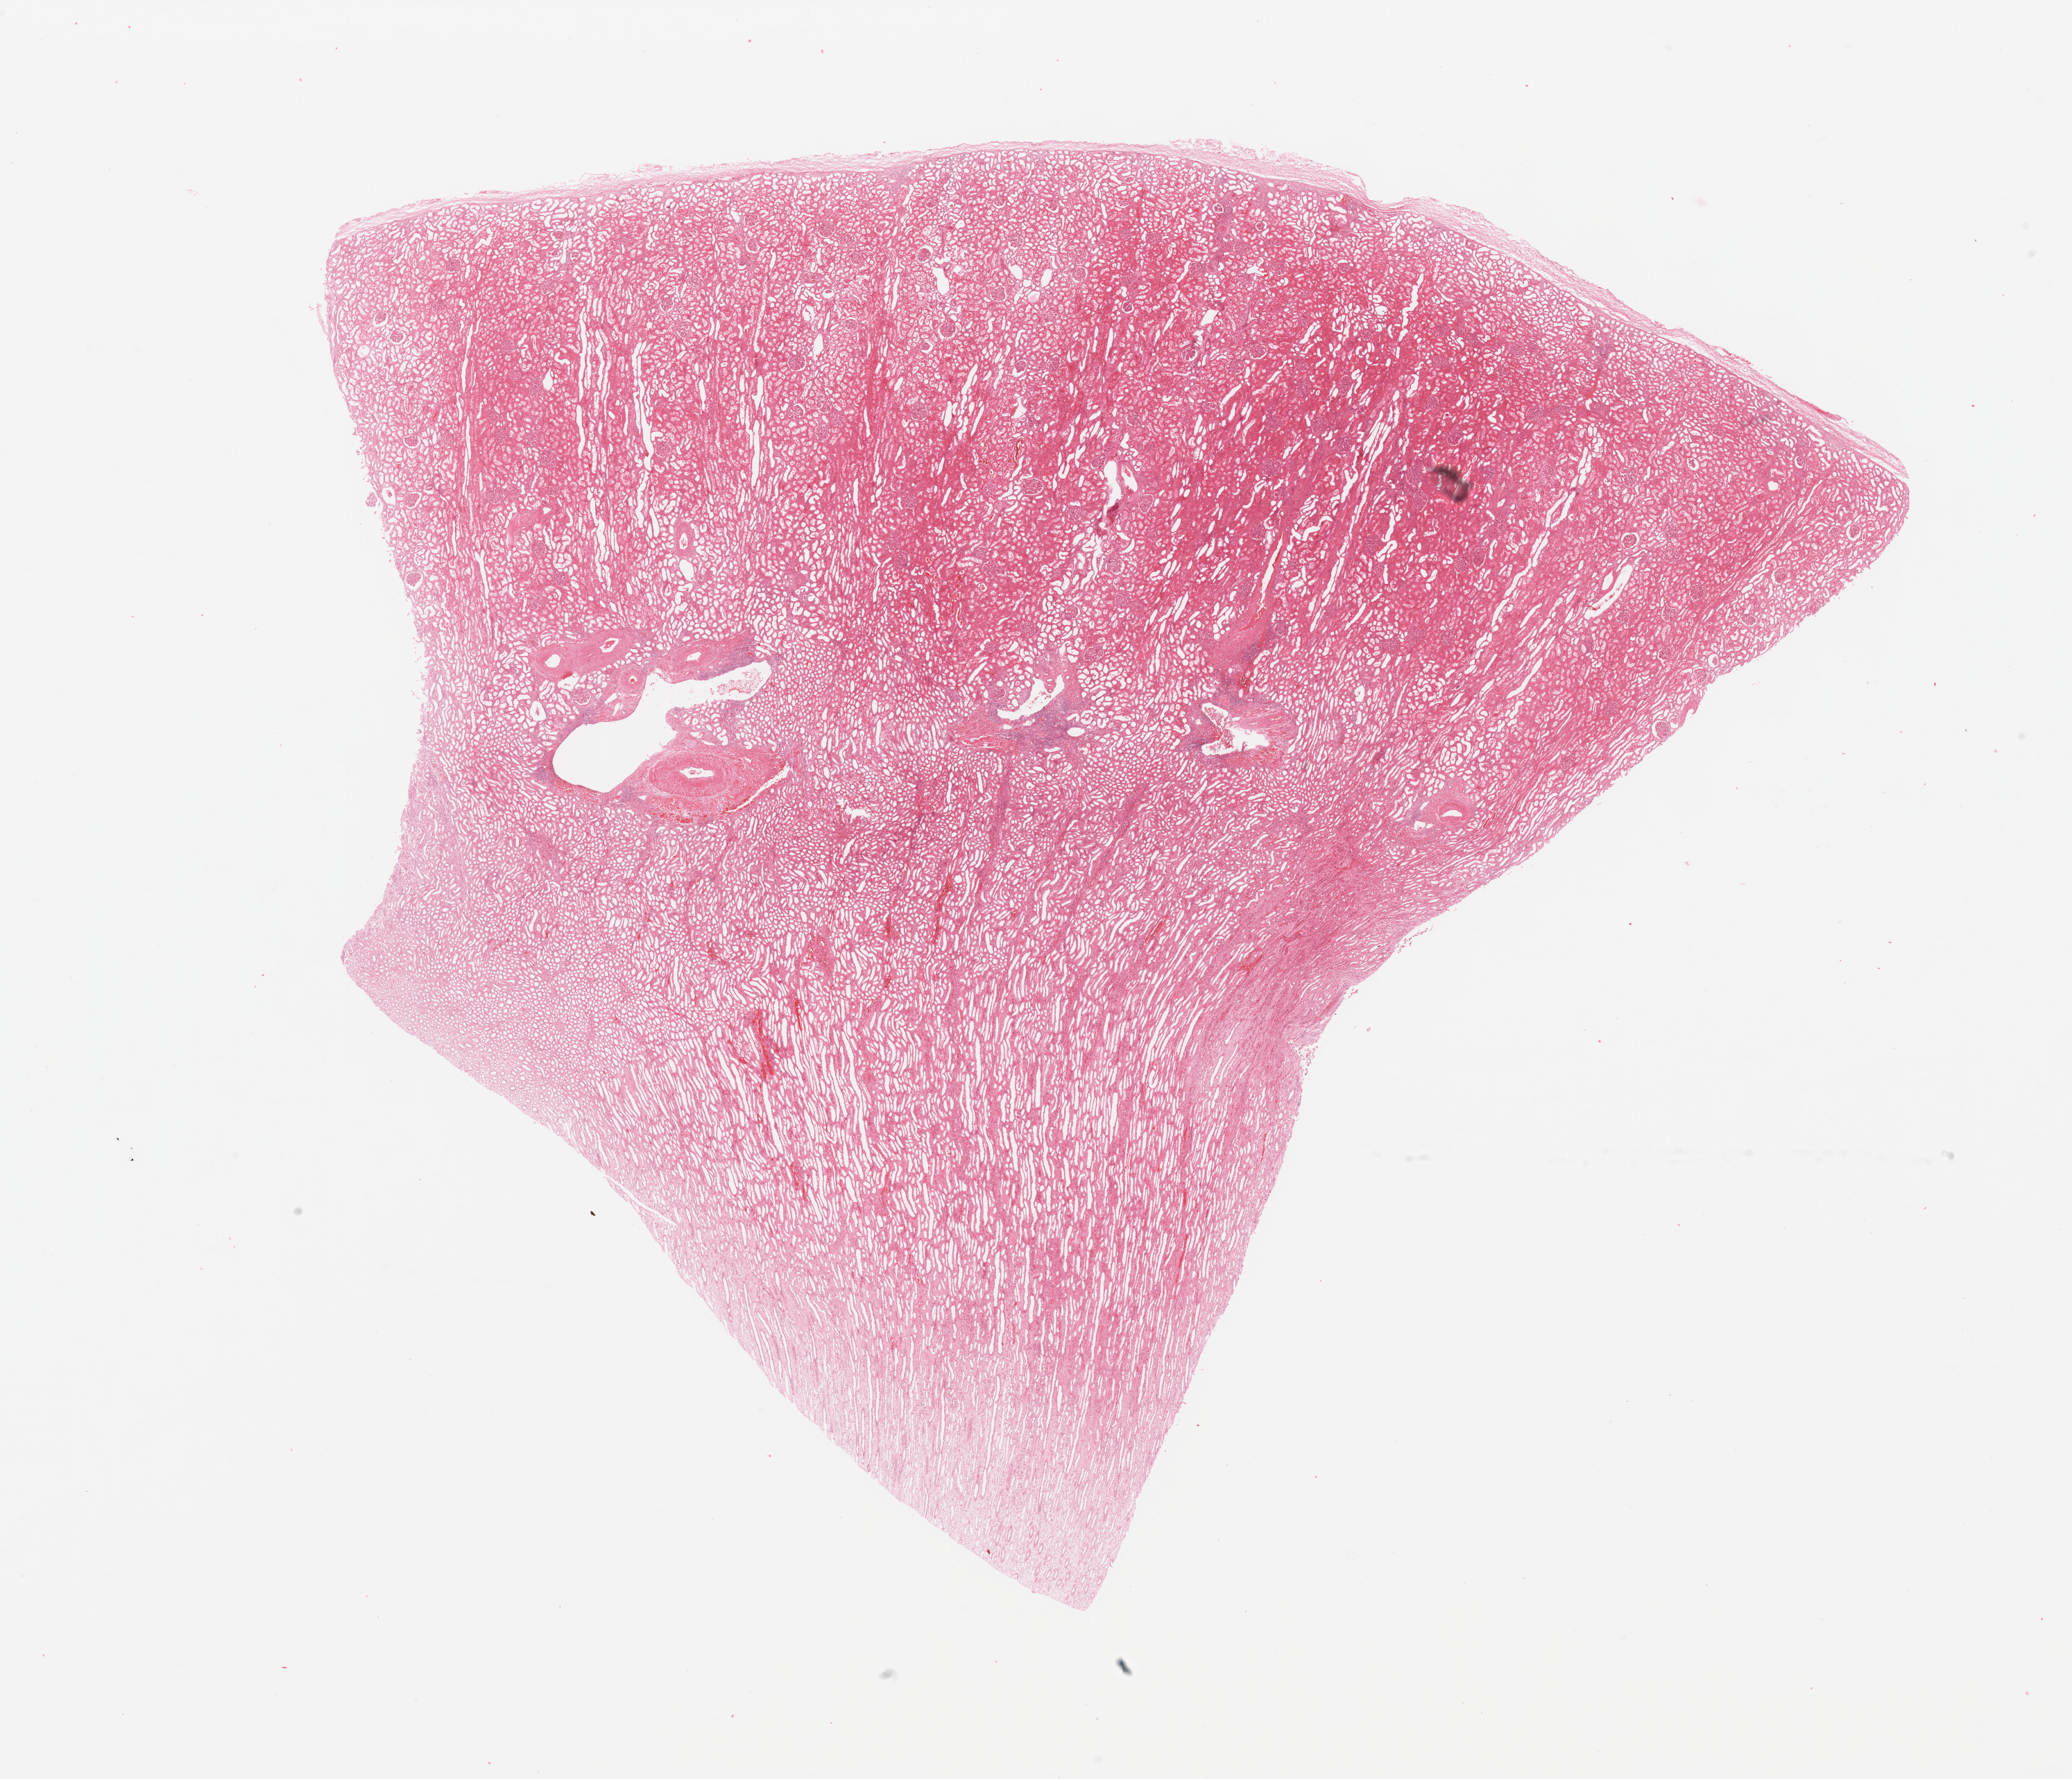
Whole-slide histology image, H&E-stained — low-resolution overview of the scanned area, about 23.6 x 20.3 mm, normal (non-tumour) tissue sample, sampled site: kidney. 52-year-old female patient.
This section: normal (non-tumour) tissue from the same patient. Patient diagnosis: Renal cell carcinoma, NOS.